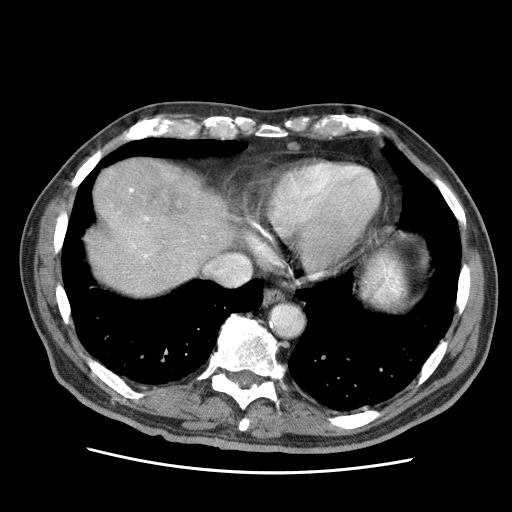
Contrast-enhanced abdominal CT (liver protocol), one axial slice; reconstruction kernel STANDARD; 120 kVp; soft-tissue window (W 400 / L 40 HU); 2.5 mm slice thickness; 512 × 512 image matrix. Case-level facts recorded for this patient, not image findings: diagnosis: hepatocellular carcinoma (patient treated with transarterial chemoembolisation; whether this scan precedes or follows treatment is not stated here); TNM stage (as recorded): Stage-IIIA; Child-Pugh class: A; tumour differentiation: well differentiated; tumour nodularity: multinodular.
Annotated regions visible in this slice (semi-automatic segmentation, software-assisted and operator-edited):
- liver parenchyma outside the tumour (the mass and vessels are separate outlines, so this box may not span the whole liver): box from (x=86, y=158) to (x=232, y=296) px
- mass: (x=144, y=177)–(x=190, y=221)
- liver vessels: (x=117, y=188)–(x=206, y=258)